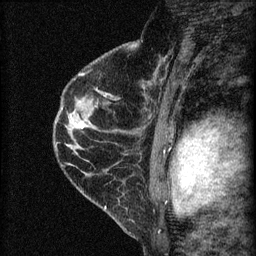
Breast MRI (dynamic contrast-enhanced), one sagittal slice. Slice 40 of 60 in the series (ordered by position). Dynamic contrast-enhanced series, image 2 of 4 at this slice position (ordered by acquisition). 1.5 T. TE 4.2 ms, TR 8.2 ms. 2 mm slice thickness. 256 × 256 image matrix, field of view 180 × 180 mm. Female patient, age 45 years.
Annotated regions visible in this slice (semi-automatically segmented with operator editing):
- analysis volume of interest (the breast-tissue region the enhancement analysis was run in; not a lesion): bounding box [x1, y1, x2, y2] px = [58, 107, 97, 147]
- tumour enhancement mask (voxels above the 70 % enhancement threshold inside the analysis volume of interest): [80, 125, 84, 128]